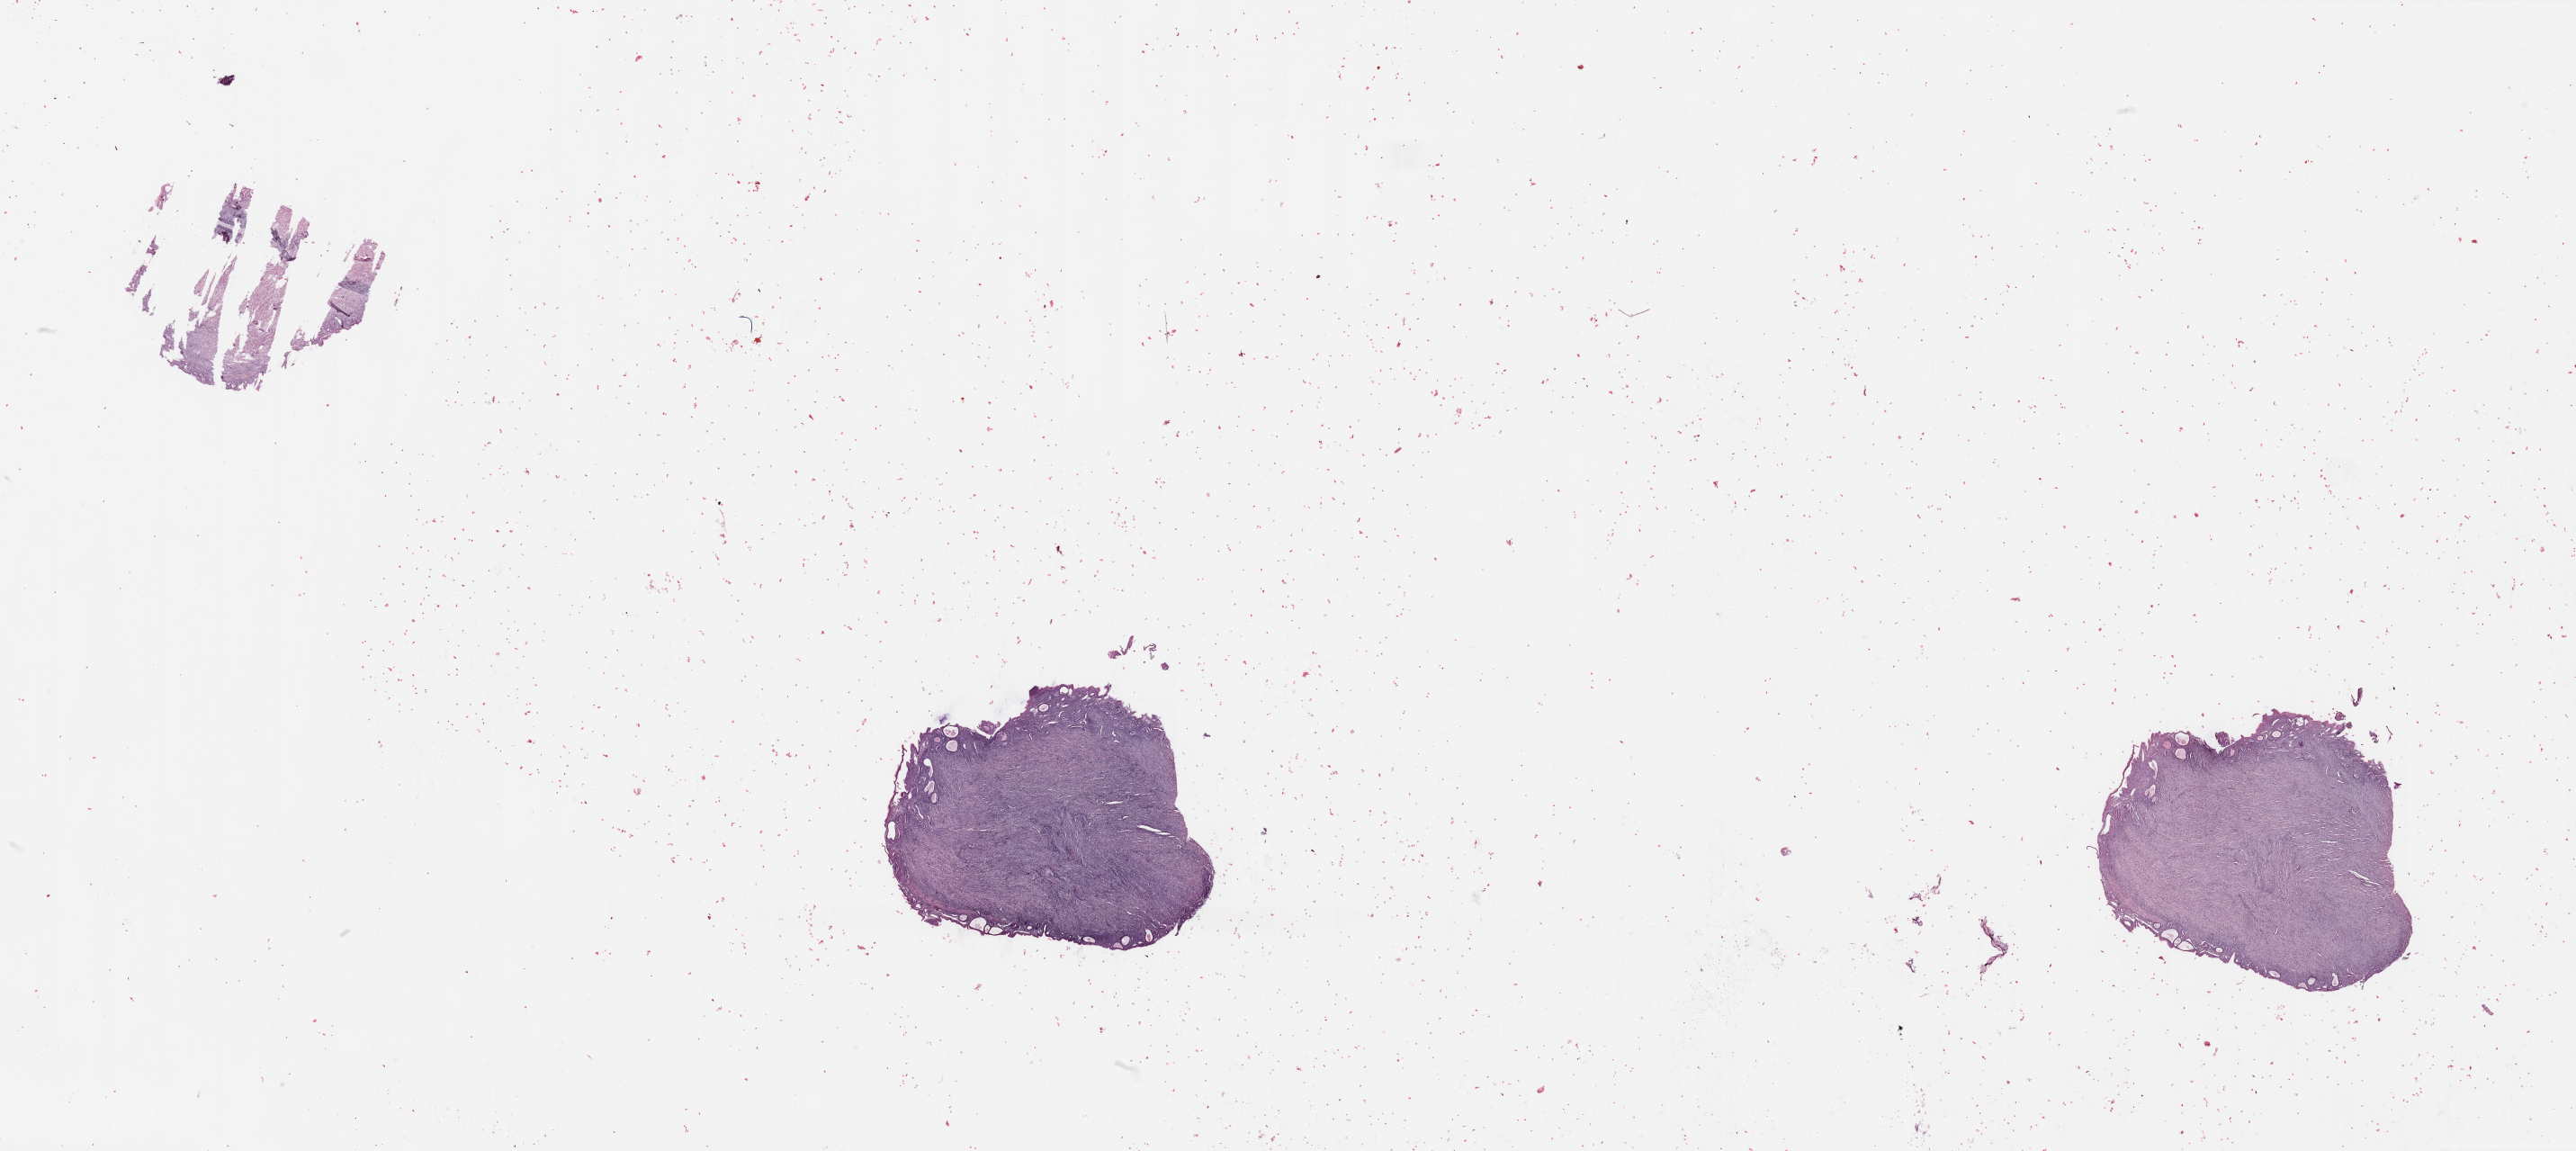
H&E-stained whole-slide image, a low-resolution overview of the entire scanned area, about 45.3 x 20.2 mm, uterus, normal (non-tumour) tissue. Patient: female, age 56 years.
* this section: normal (non-tumour) tissue from the same patient
* patient diagnosis: Endometrioid adenocarcinoma, NOS